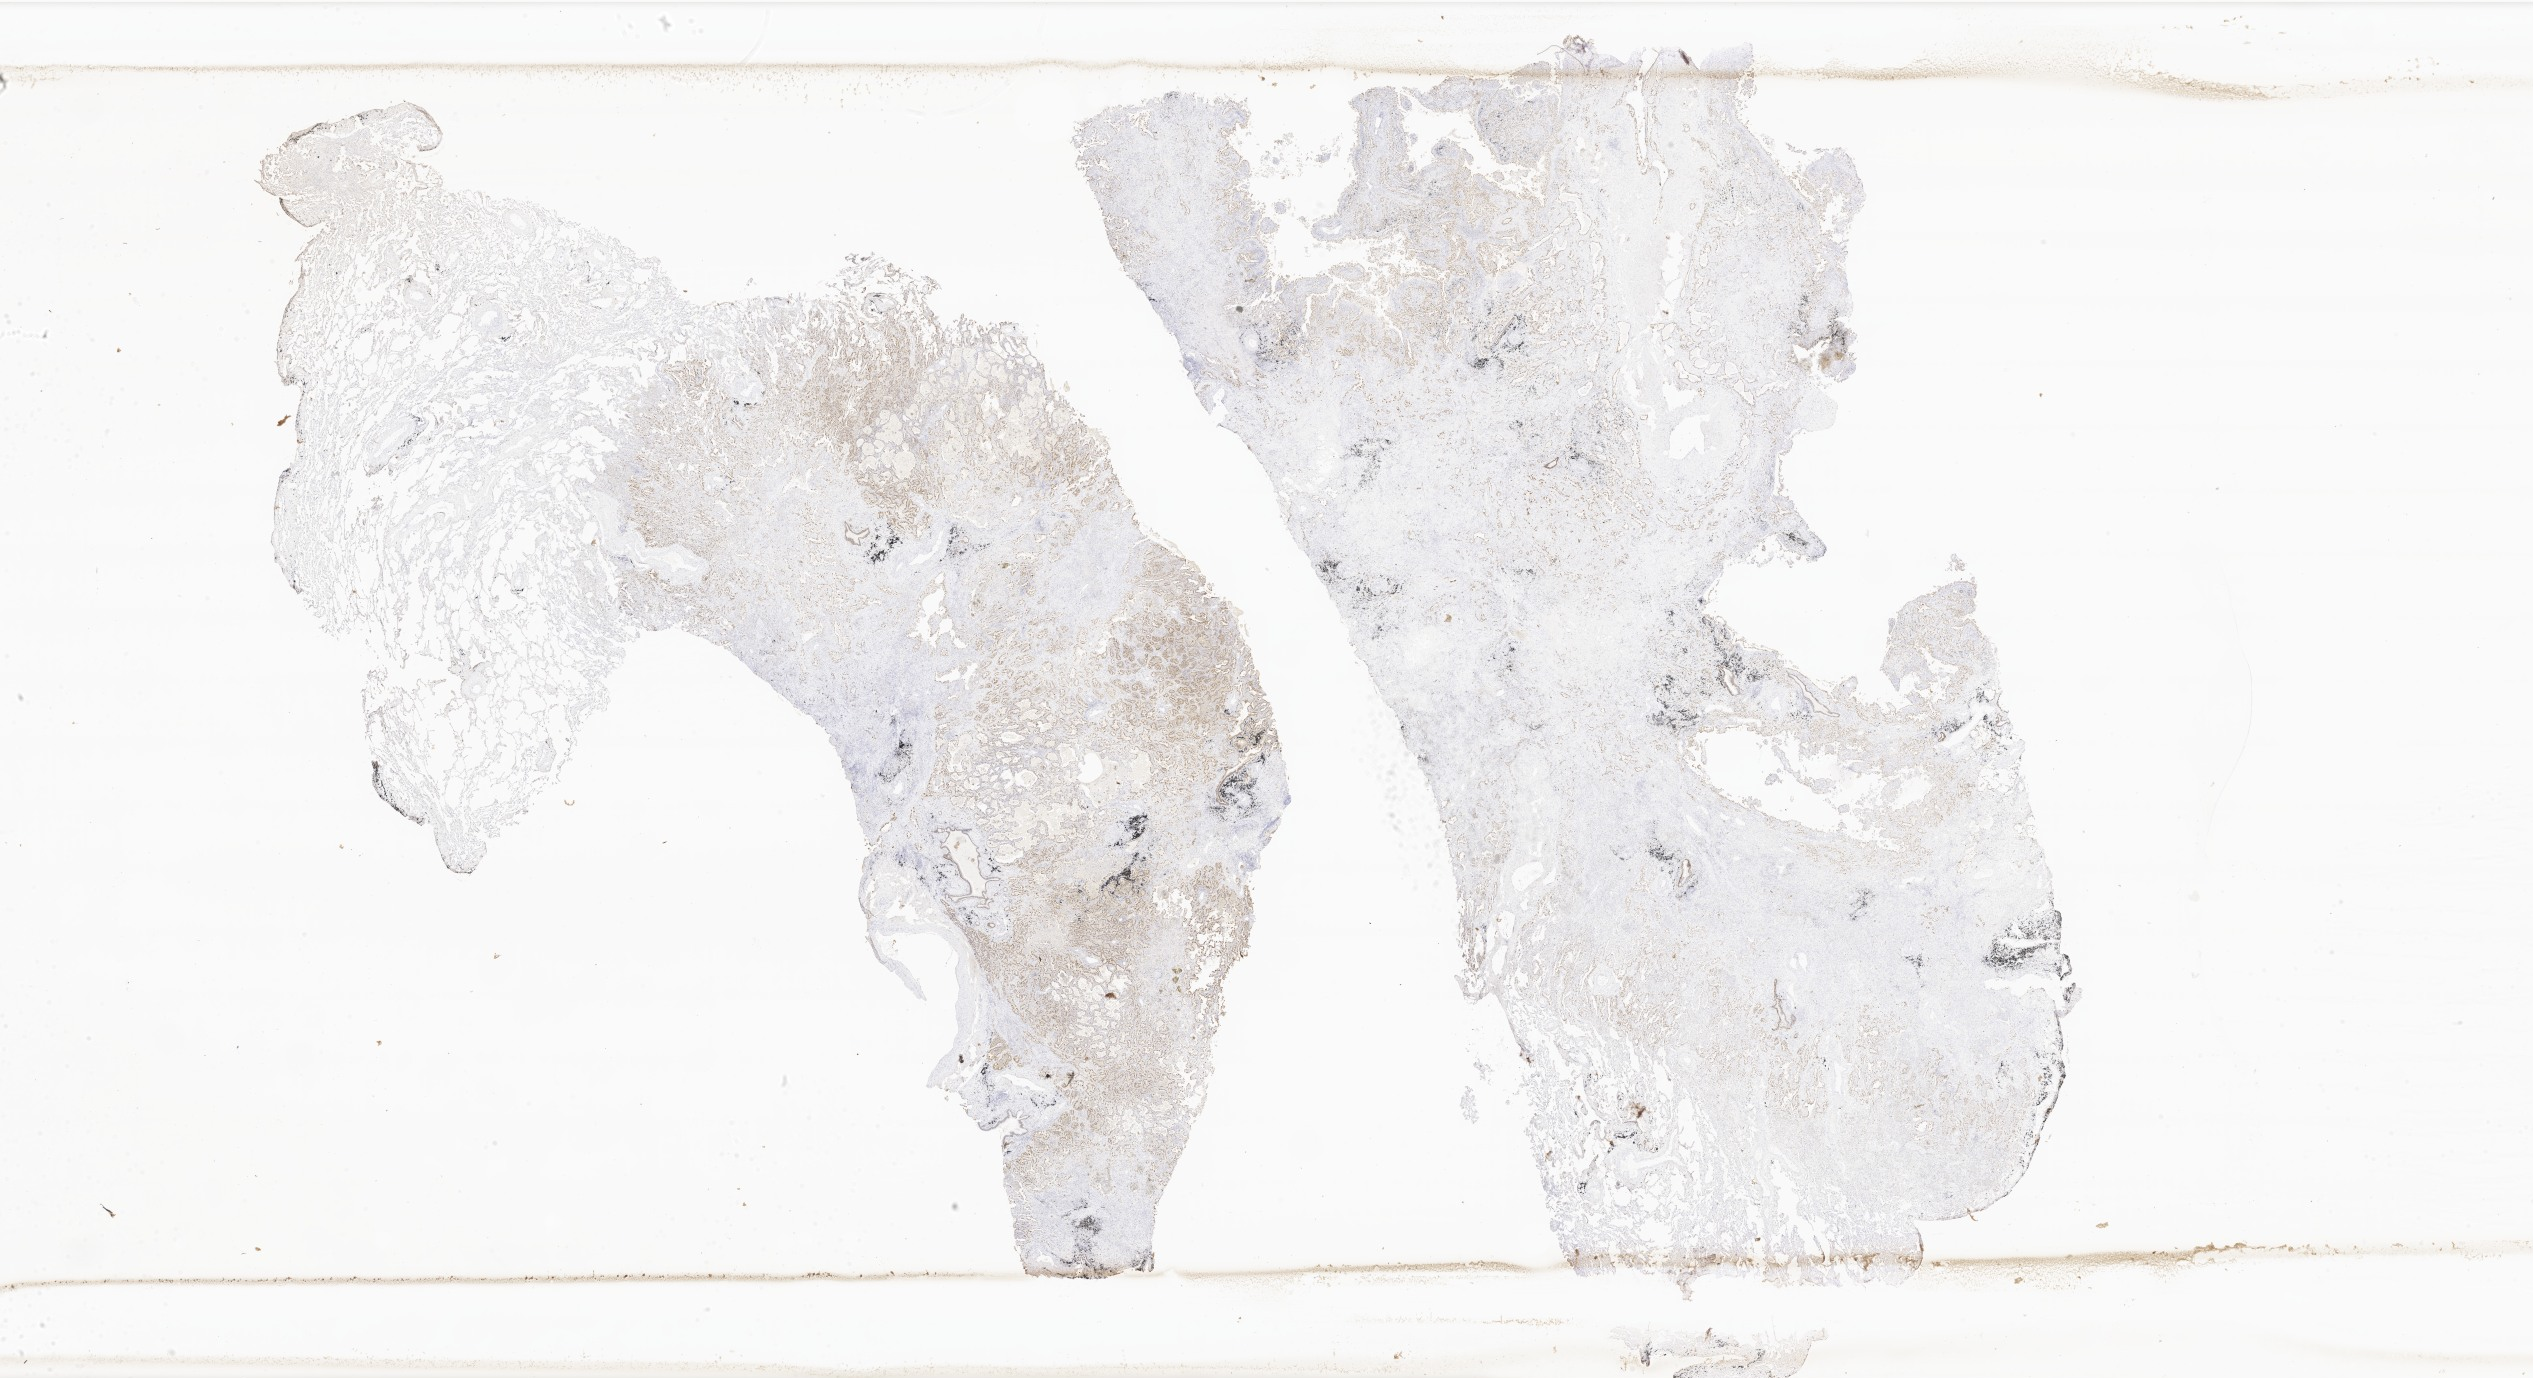
Immunohistochemistry (IHC) whole-slide image stained for TTF-1 (thyroid transcription factor 1) — whole scanned area (about 42.7 x 23.2 mm) shown as a low-resolution overview, tumor tissue, anatomic site: lung (right). Patient male; age 69 years.
Diagnosis: Non-small cell carcinoma.